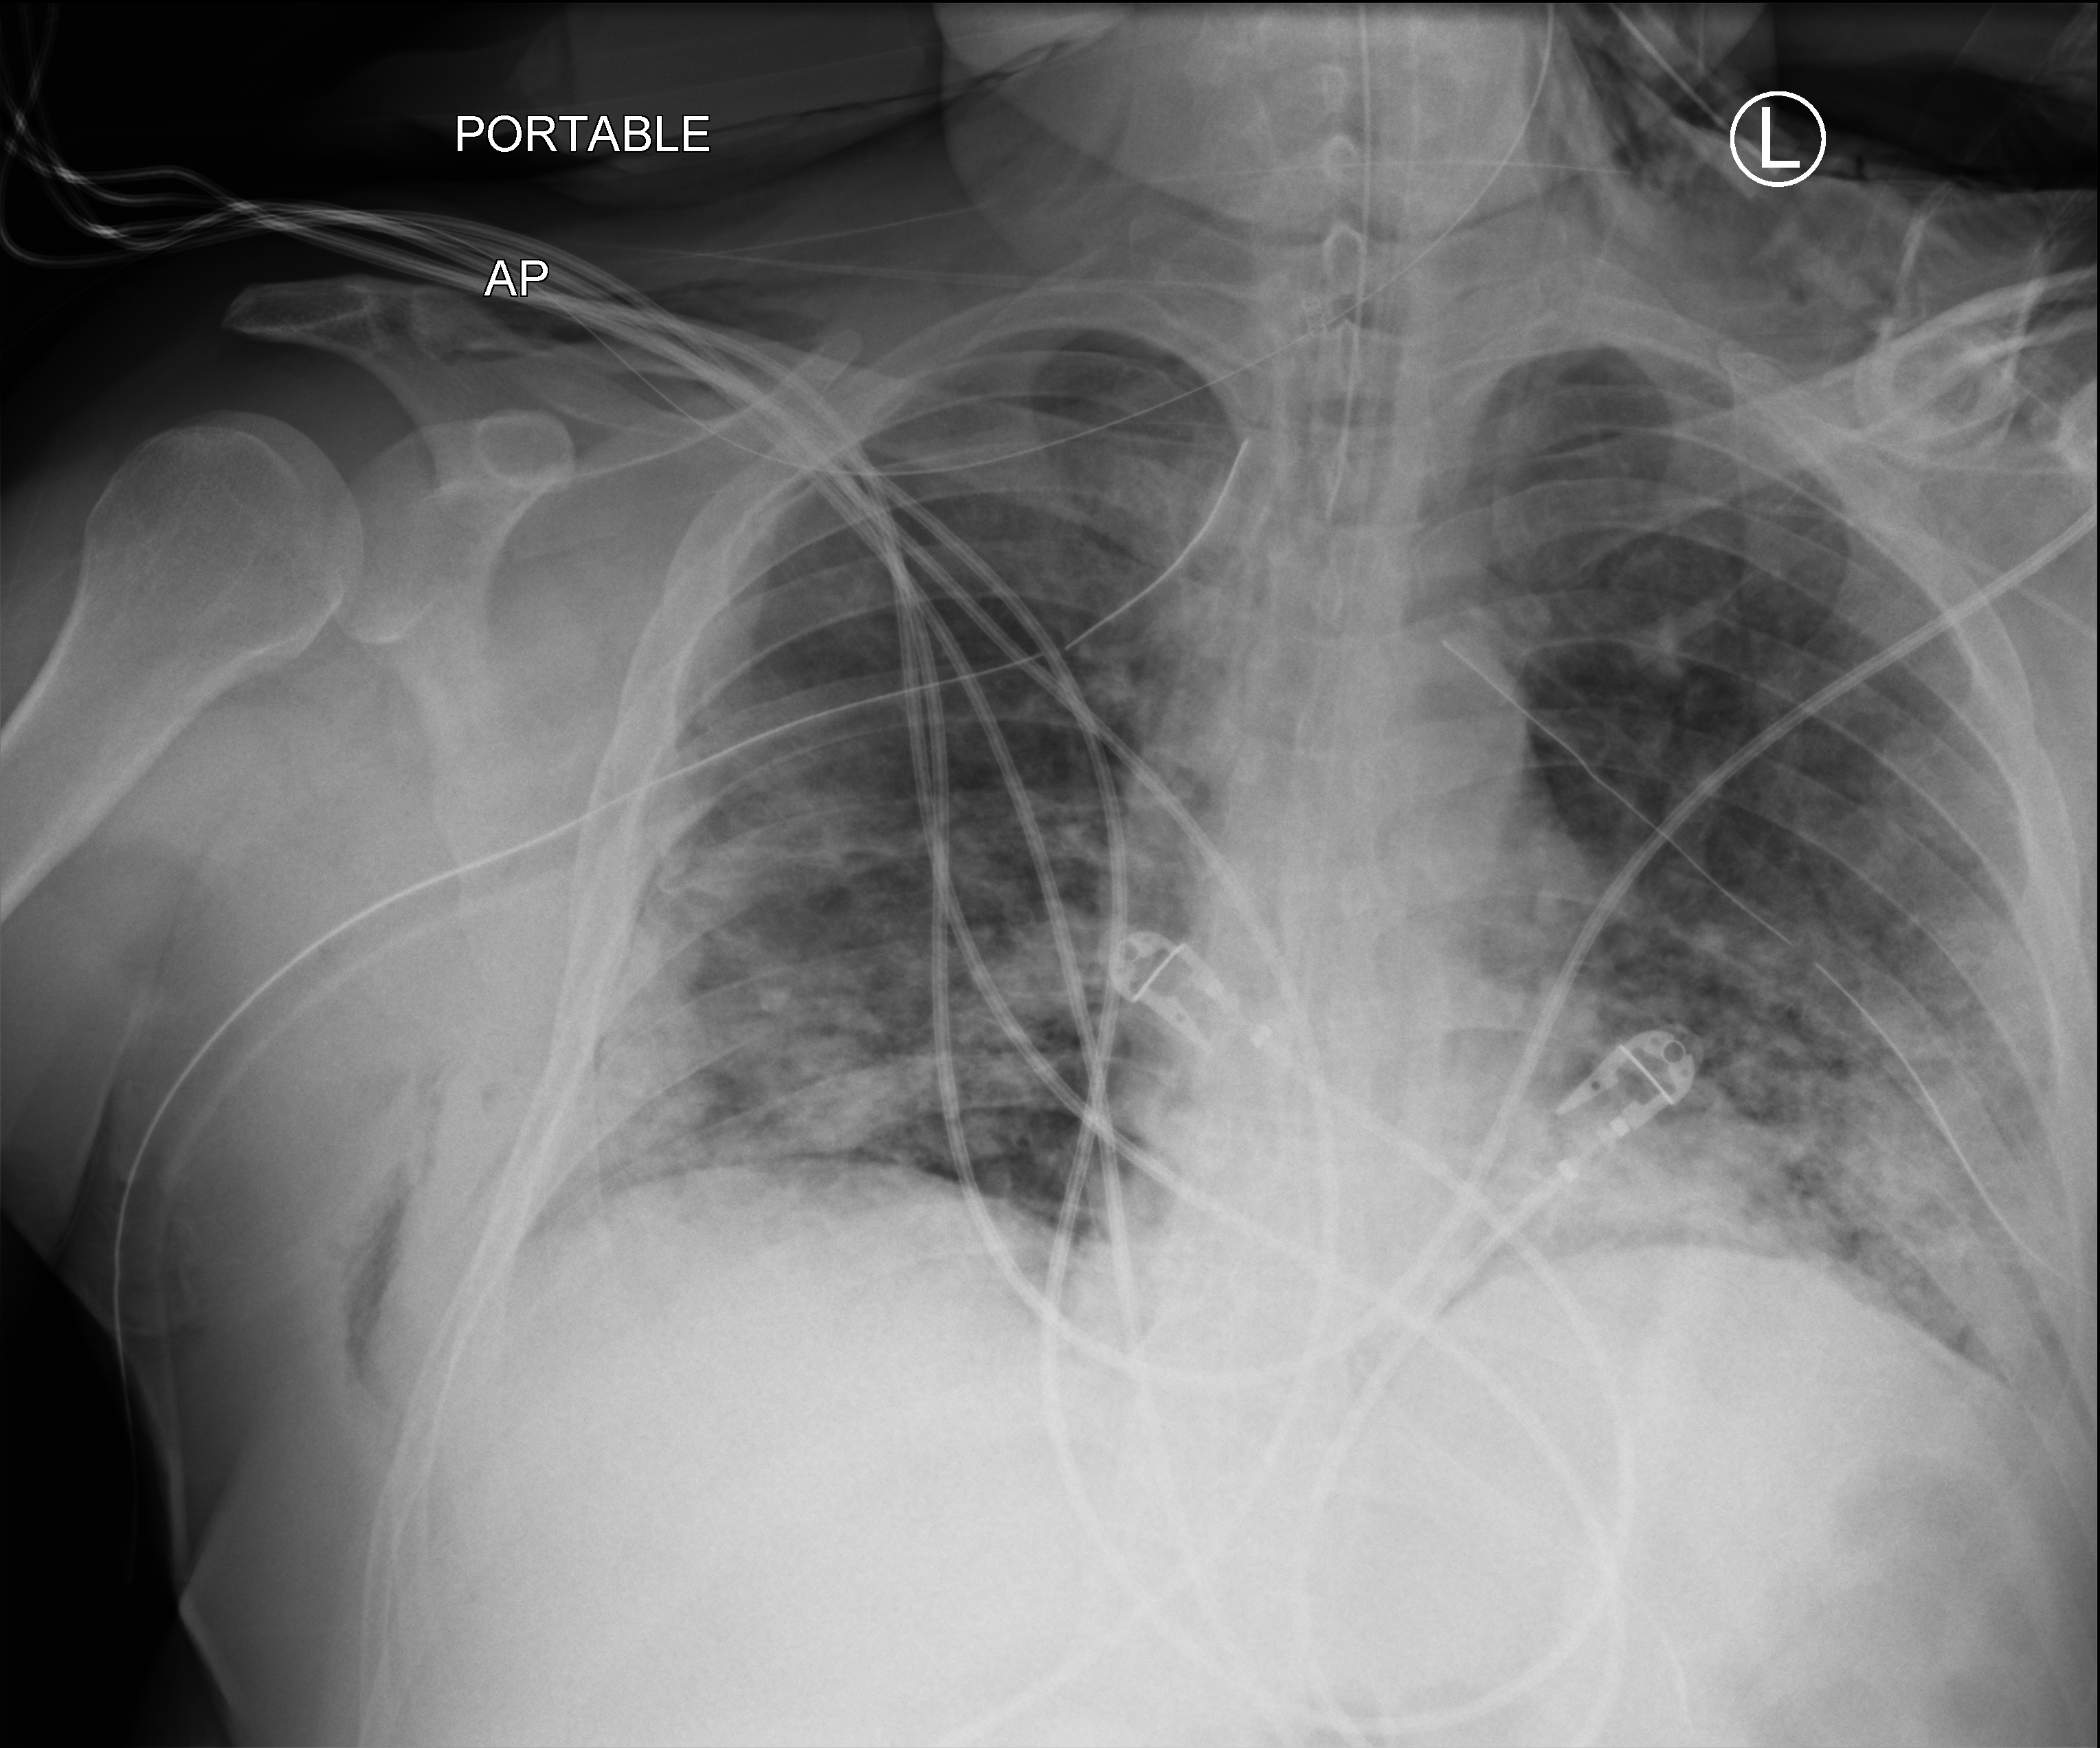
Bedside chest radiograph (computed radiography); anteroposterior (AP) projection. Male patient hospitalised with COVID-19, age 18–59 years.
Hospital-stay facts (about this admission, not read from this image; timing relative to this image not recorded): mechanically ventilated during this hospital stay: yes; diabetes (admission record): yes; admitted to intensive care during this hospital stay: yes.